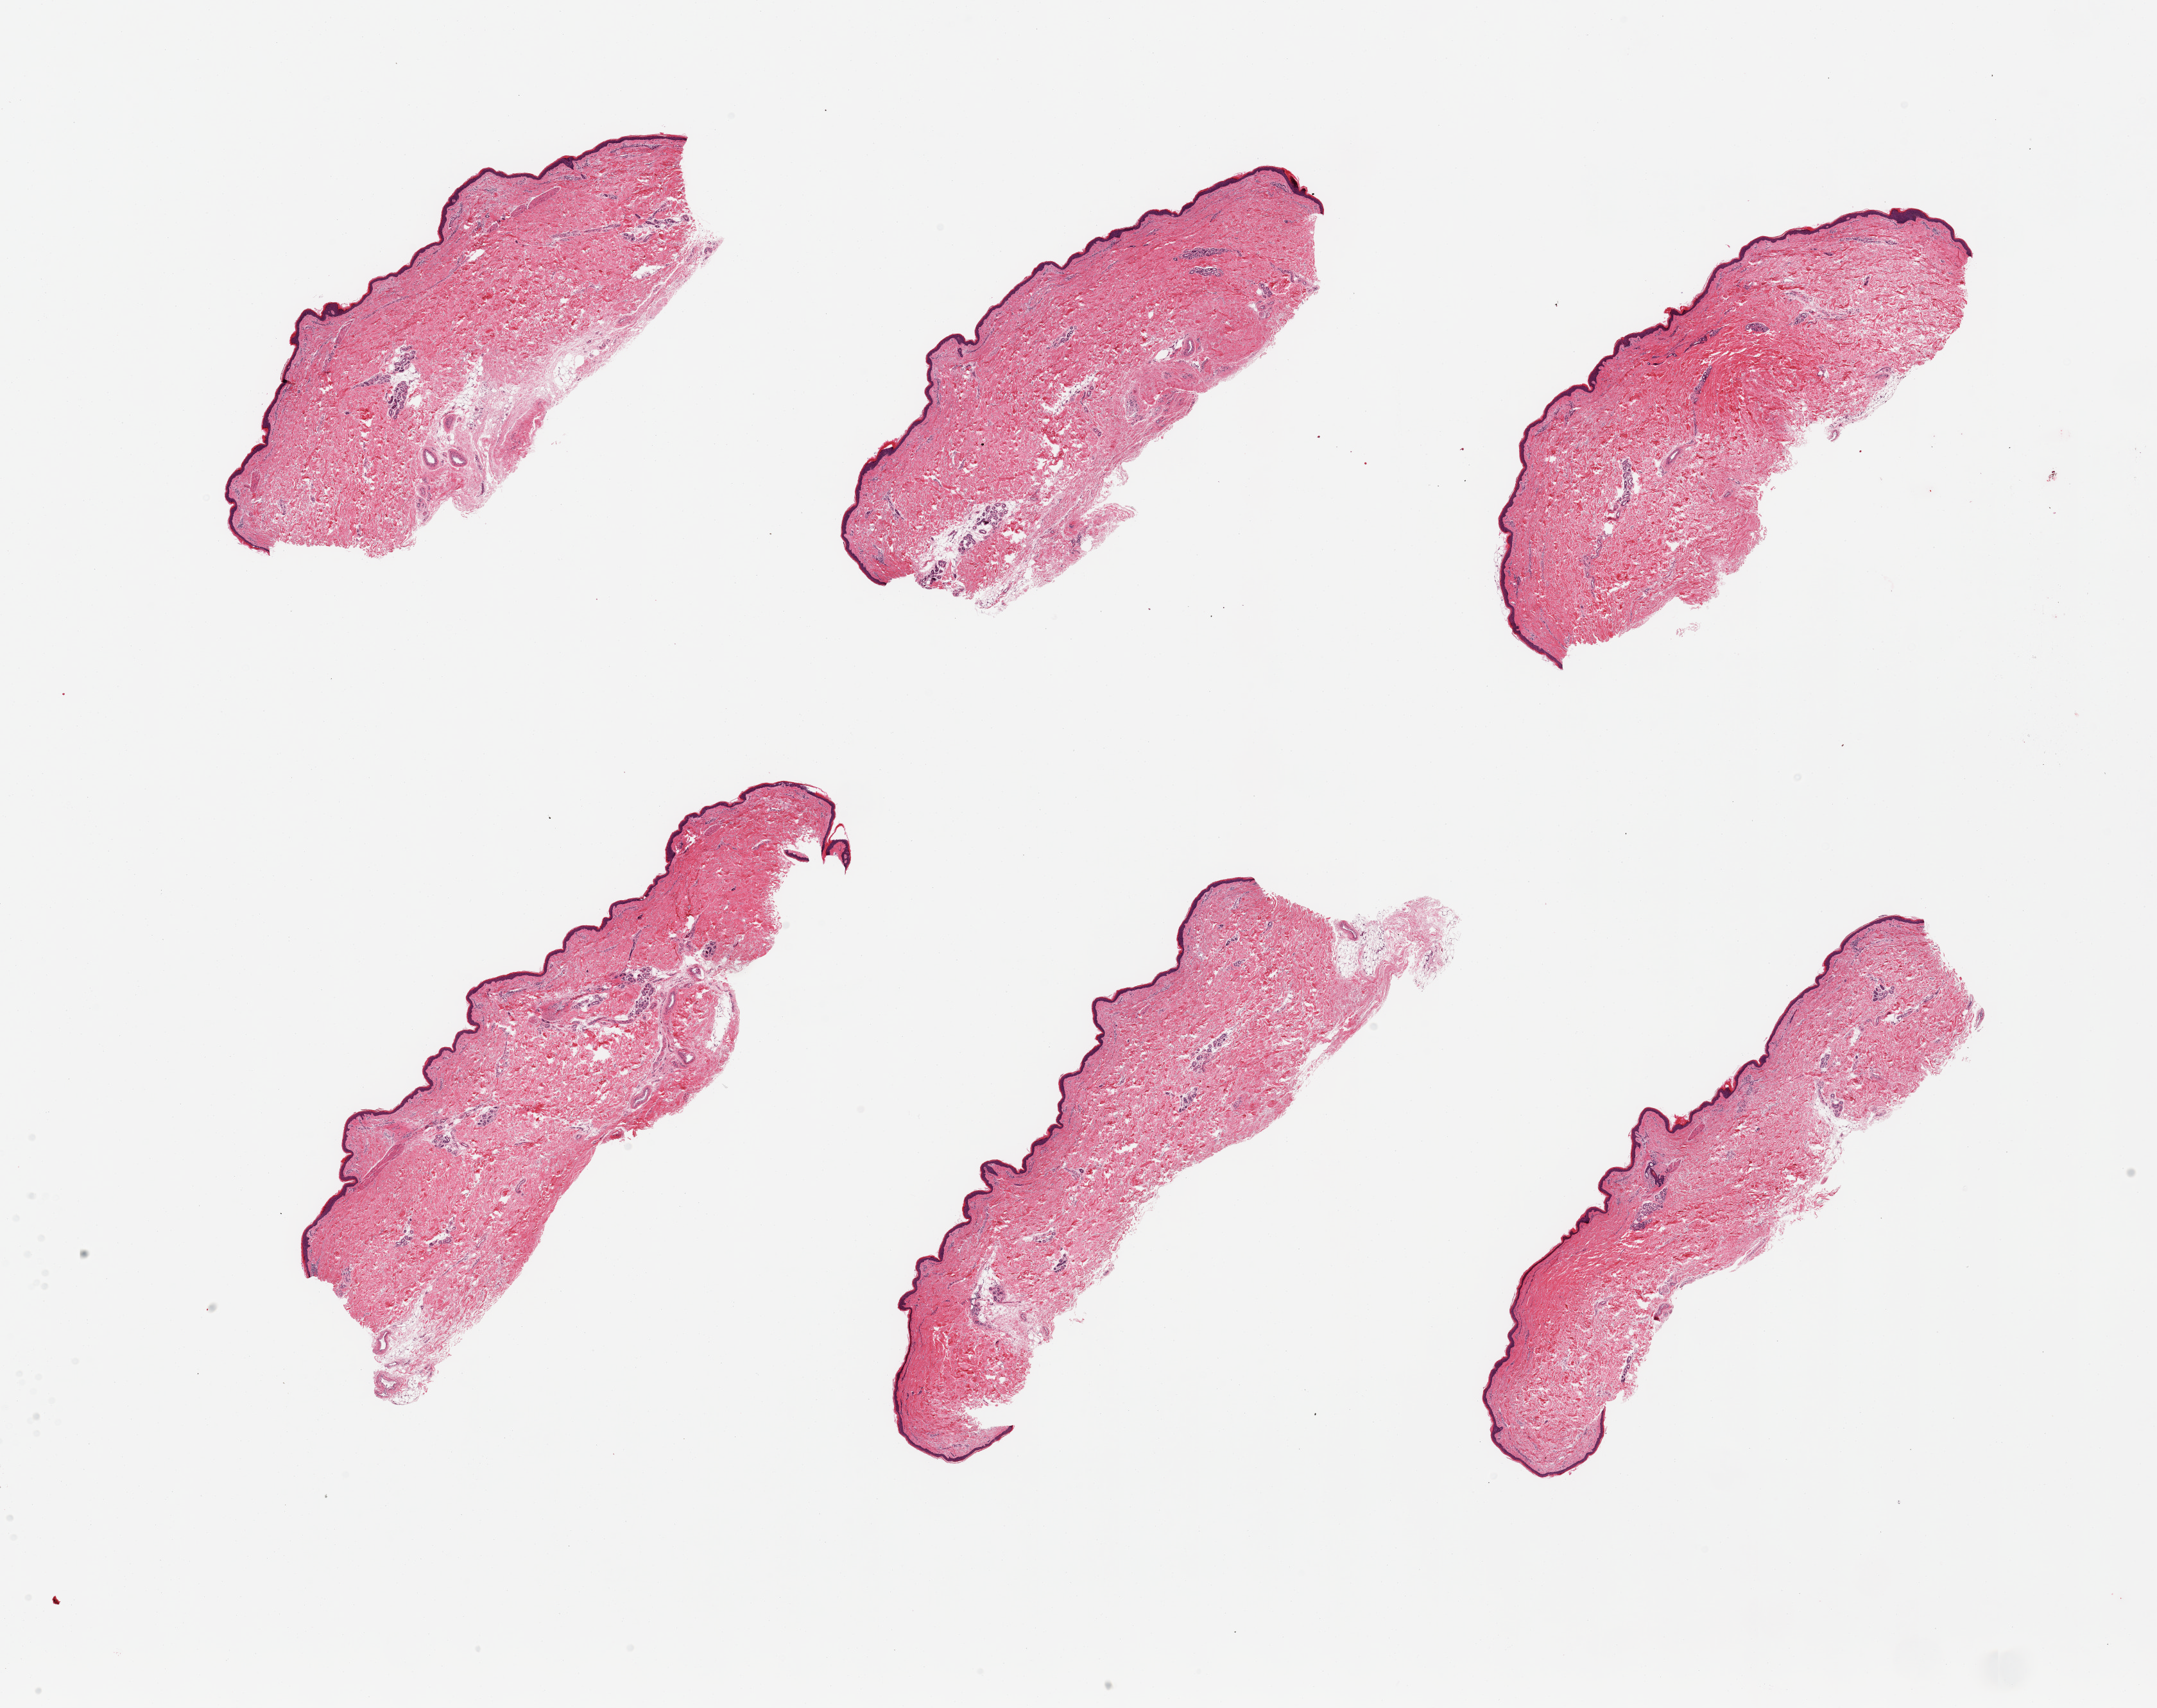
H&E whole-slide image, shown as a low-resolution overview of the whole scanned area (about 26.6 x 21.1 mm, slide scanned at 20x); PAXgene-fixed, paraffin-embedded tissue; section of skin of lower leg (target tissue); donor tissue sample.
• review note (as recorded): 6 pieces; well trimmed, <5% dermal fat